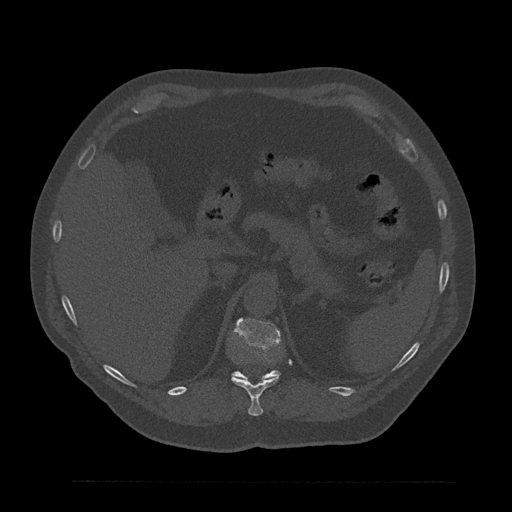
CT including the spine, one axial slice; slice 266 of 797 in the series (ordered by position); reconstruction kernel Br40s/3; 120 kVp; bone window (W 1800 / L 400 HU); 0.5 mm slice thickness; 512 × 512 image matrix, field of view 430 × 430 mm. Male patient, age 61 years. Case-level facts recorded for this patient, not image findings: primary cancer: prostate.
Outlined on this slice (semi-automatically segmented with operator editing):
- L1 vertebra: bounding box [x1, y1, x2, y2] px = [265, 375, 280, 380]
- T11 vertebra: [231, 375, 279, 416]
- T12 vertebra: [232, 318, 280, 380]